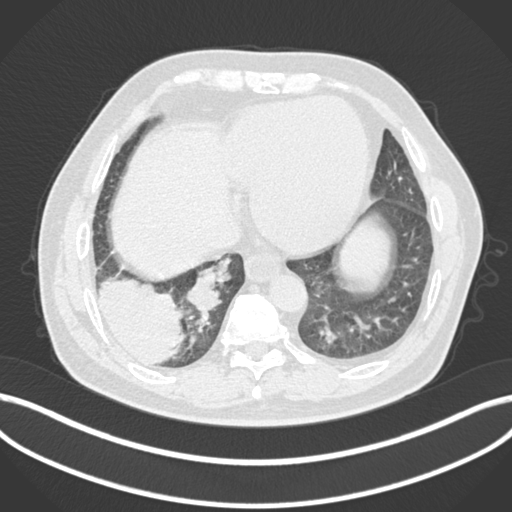
Chest CT, one axial slice. Slice 36 of 200 in the series (ordered by position). Reconstruction kernel B30f. 120 kVp. Lung window (W 1500 / L -600 HU). 1 mm slice thickness. 512 × 512 image matrix. Patient: male, 59 years.
Annotated regions visible in this slice (rectangle marked by the reading radiologist):
- lung tumour (recorded histology: adenocarcinoma): bounding box [x1, y1, x2, y2] px = [97, 271, 186, 368]